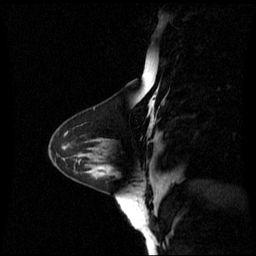
Breast MRI (dynamic contrast-enhanced), one sagittal slice; position 23 of 60 along the scan axis; dynamic contrast-enhanced series, image 2 of 3 at this slice position (ordered by acquisition); 1.5 T; TE 4.2 ms, TR 8.4 ms; 2.4 mm slice thickness; 256 × 256 image matrix, field of view 250 × 250 mm. Female patient, age 44 years. From the clinical record (not read from this slice): setting: breast cancer imaged before/during neoadjuvant chemotherapy; receptor status: triple-negative.
Structures marked on this image (semi-automatically segmented with operator editing):
- analysis volume of interest (the breast-tissue region the enhancement analysis was run in; not a lesion): bounding box (x1, y1, x2, y2) in pixels: (79, 148, 132, 190)
- tumour enhancement mask (voxels above the 70 % enhancement threshold inside the analysis volume of interest): (109, 168, 112, 171)